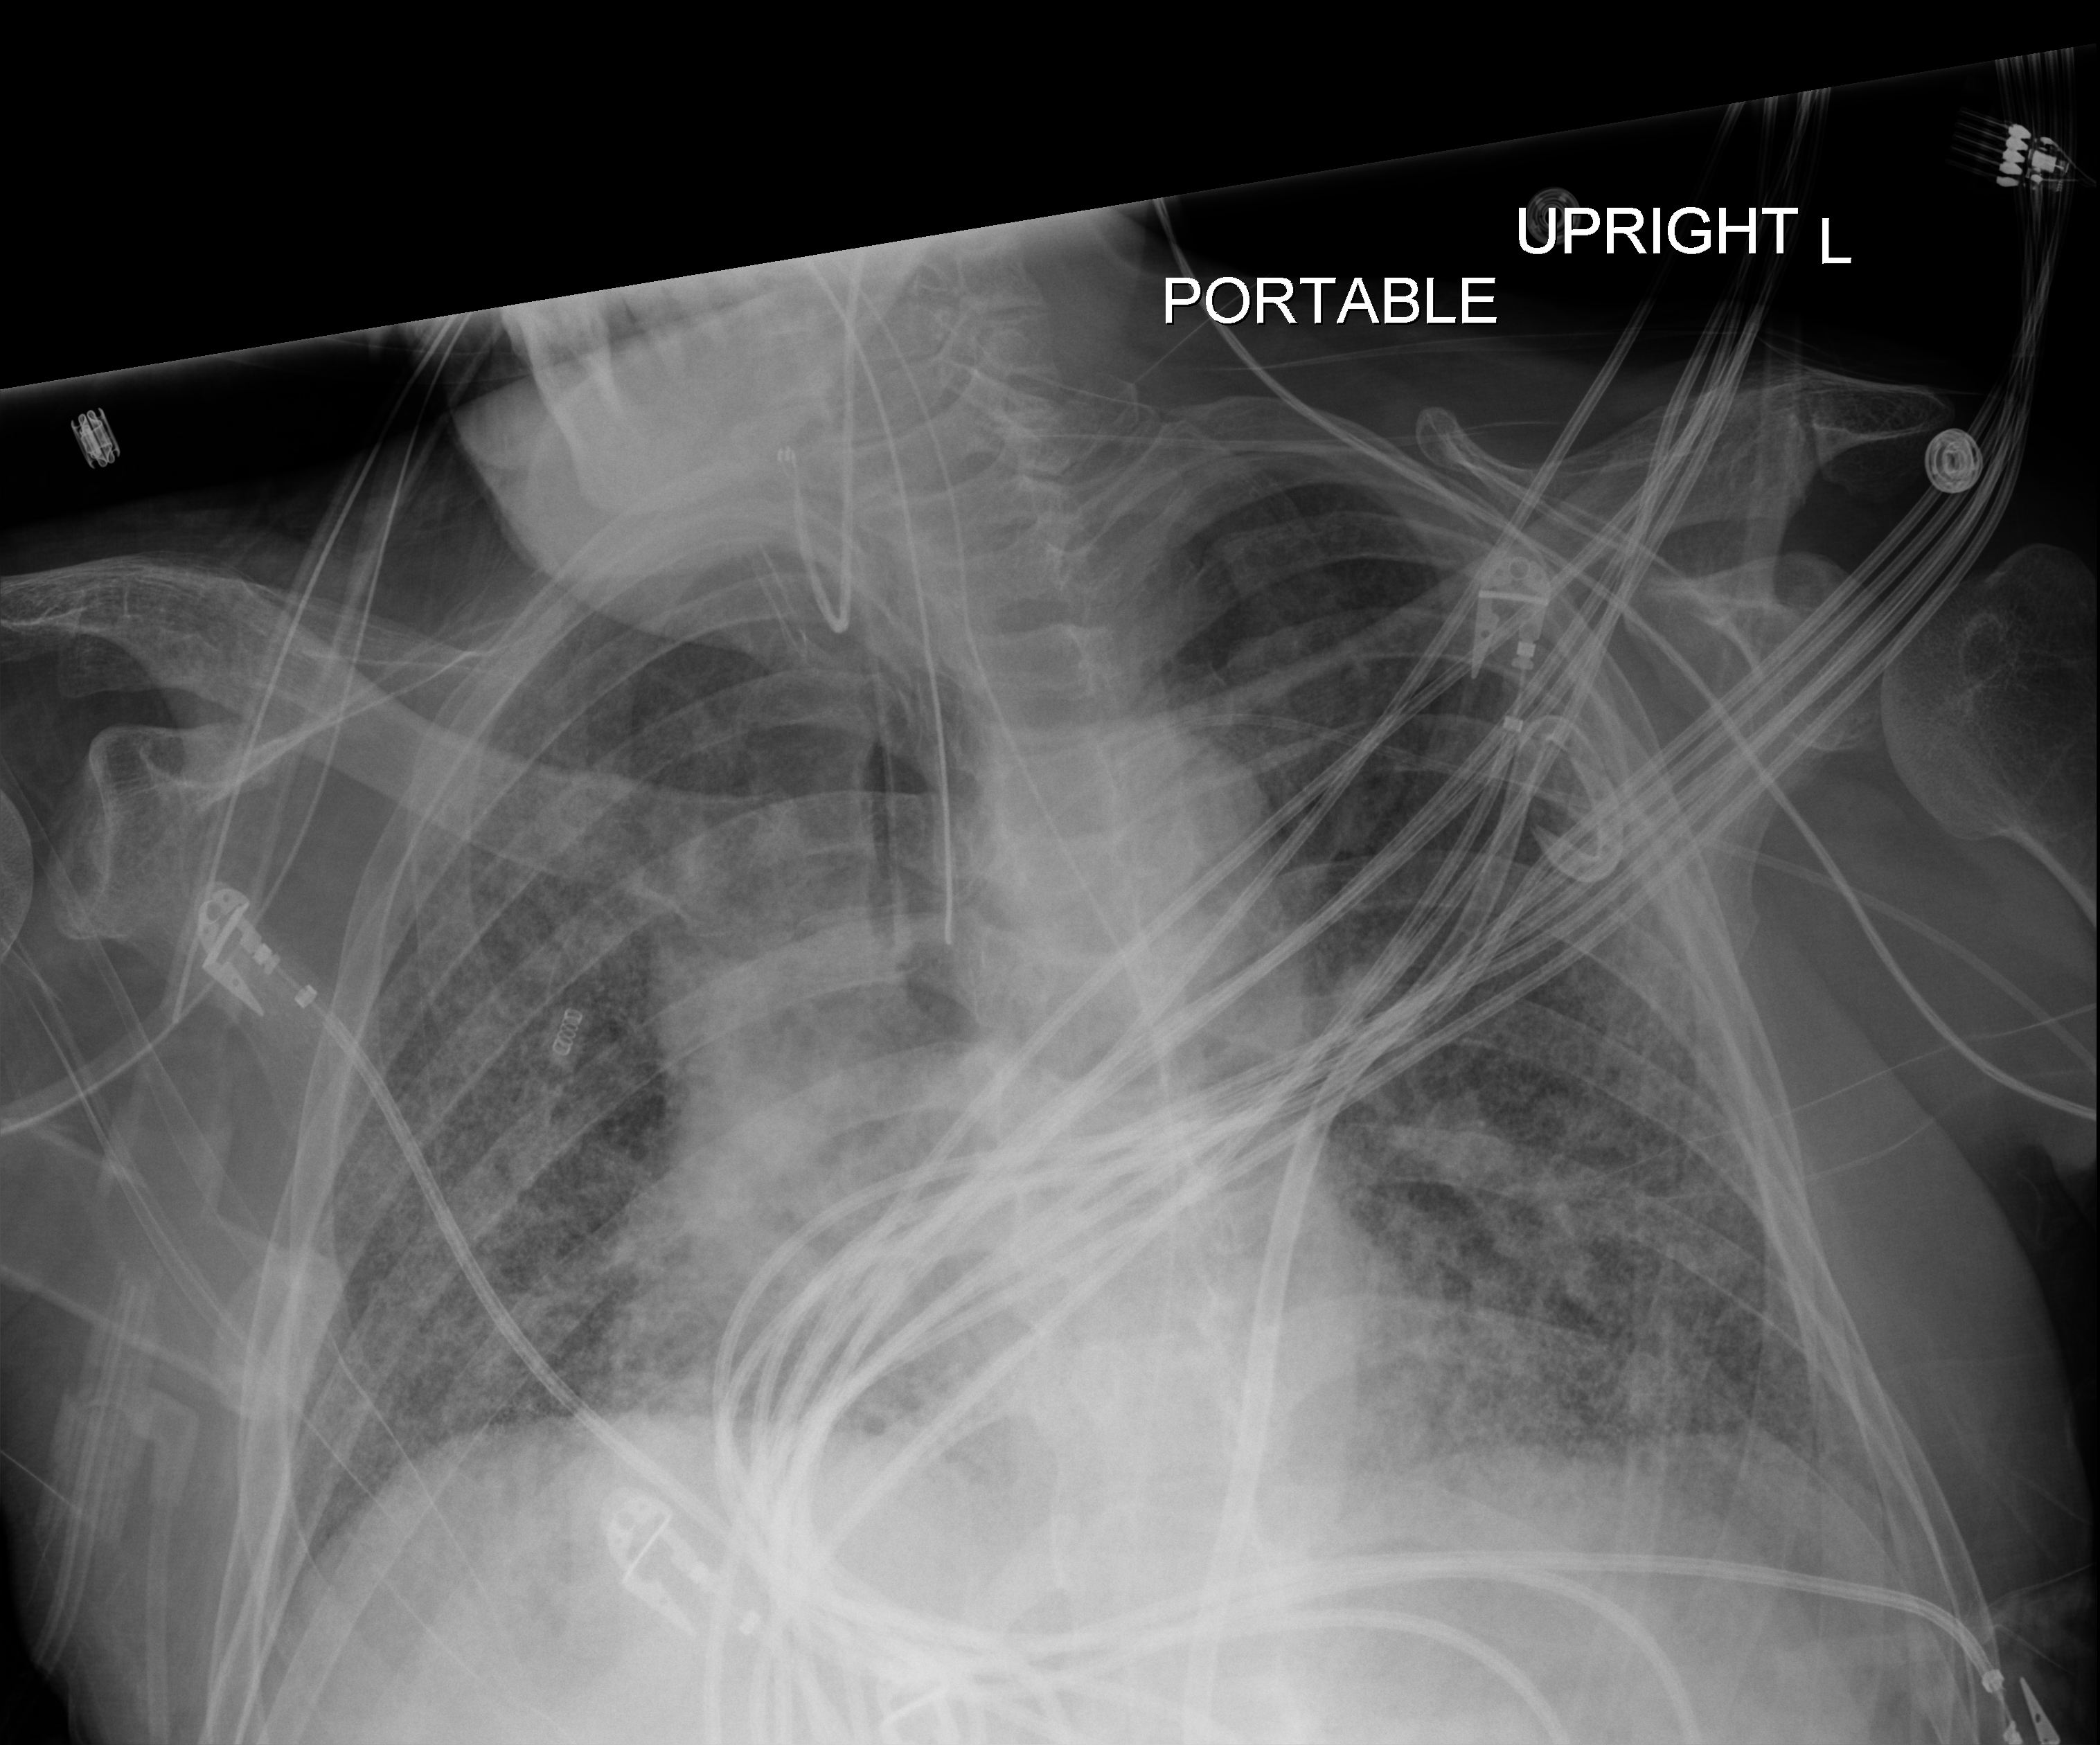
Chest radiograph (digital radiography). Patient hospitalised with COVID-19; male, aged 60–74 years.
Hospital-stay facts (about this admission, not read from this image; timing relative to this image not recorded): length of hospital stay: 54 days; admitted to intensive care during this hospital stay: yes.